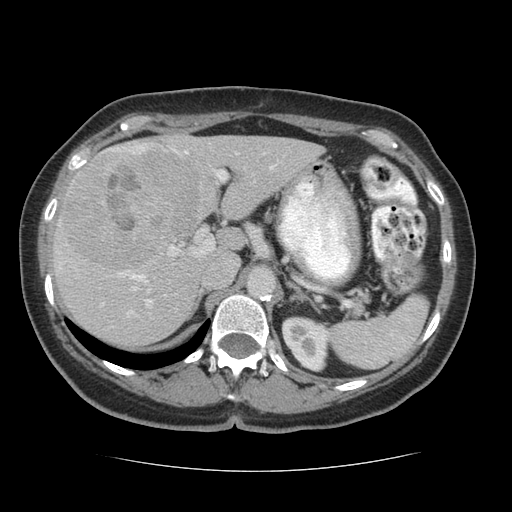
Contrast-enhanced abdominal CT (liver protocol), one axial slice. Position 40 of 75 along the scan axis. Reconstruction kernel STANDARD. Soft-tissue window (W 400 / L 40 HU). 2.5 mm slice thickness. 512 × 512 image matrix, field of view 360 × 360 mm. Case-level facts recorded for this patient, not image findings: diagnosis: hepatocellular carcinoma (patient treated with transarterial chemoembolisation; whether this scan precedes or follows treatment is not stated here); TNM stage (as recorded): Stage-I; Child-Pugh class: A; tumour nodularity: uninodular.
Annotated regions visible in this slice (semi-automatically segmented with operator editing):
- liver parenchyma outside the tumour (the mass and vessels are separate outlines, so this box may not span the whole liver): box from (x=52, y=132) to (x=322, y=346) px
- mass: (x=61, y=147)–(x=199, y=272)
- liver vessels: (x=57, y=143)–(x=276, y=317)